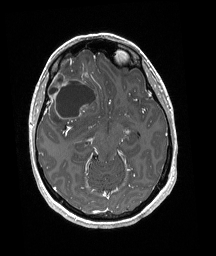
Brain MRI from a brain-tumour surgery series, one axial slice. Position 114 of 192 along the scan axis. T1-weighted post-contrast. 216 × 256 image matrix. From the clinical record (not read from this slice): histopathology: Oligodendroglioma; WHO grade: 3; IDH mutation: yes; tumour location: Right Frontal.
Annotated regions visible in this slice (expert manual segmentation):
- tumour: box from (x=46, y=54) to (x=97, y=125) px